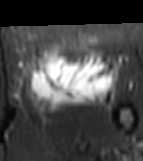
MRI of an extremity soft-tissue mass, one axial slice; slice 35 of 81 in the series (ordered by position); STIR; MR volume resampled by the dataset authors to the PET/CT grid (not the native acquisition matrix); 3.27 mm slice thickness; 143 × 161 image matrix, field of view 140 × 157 mm. Female patient. Case-level facts recorded for this patient, not image findings: histological type: myxofibrosarcoma; grade: intermediate; site of the primary tumour: left thigh.
Annotated regions visible in this slice (expert contour drawn on MRI and transferred to this co-registered scan by the dataset authors):
- gross tumour volume including surrounding oedema: bounding box <26,44,118,116> (left, top, right, bottom; pixels)
- gross tumour volume (mass): <29,44,112,100>